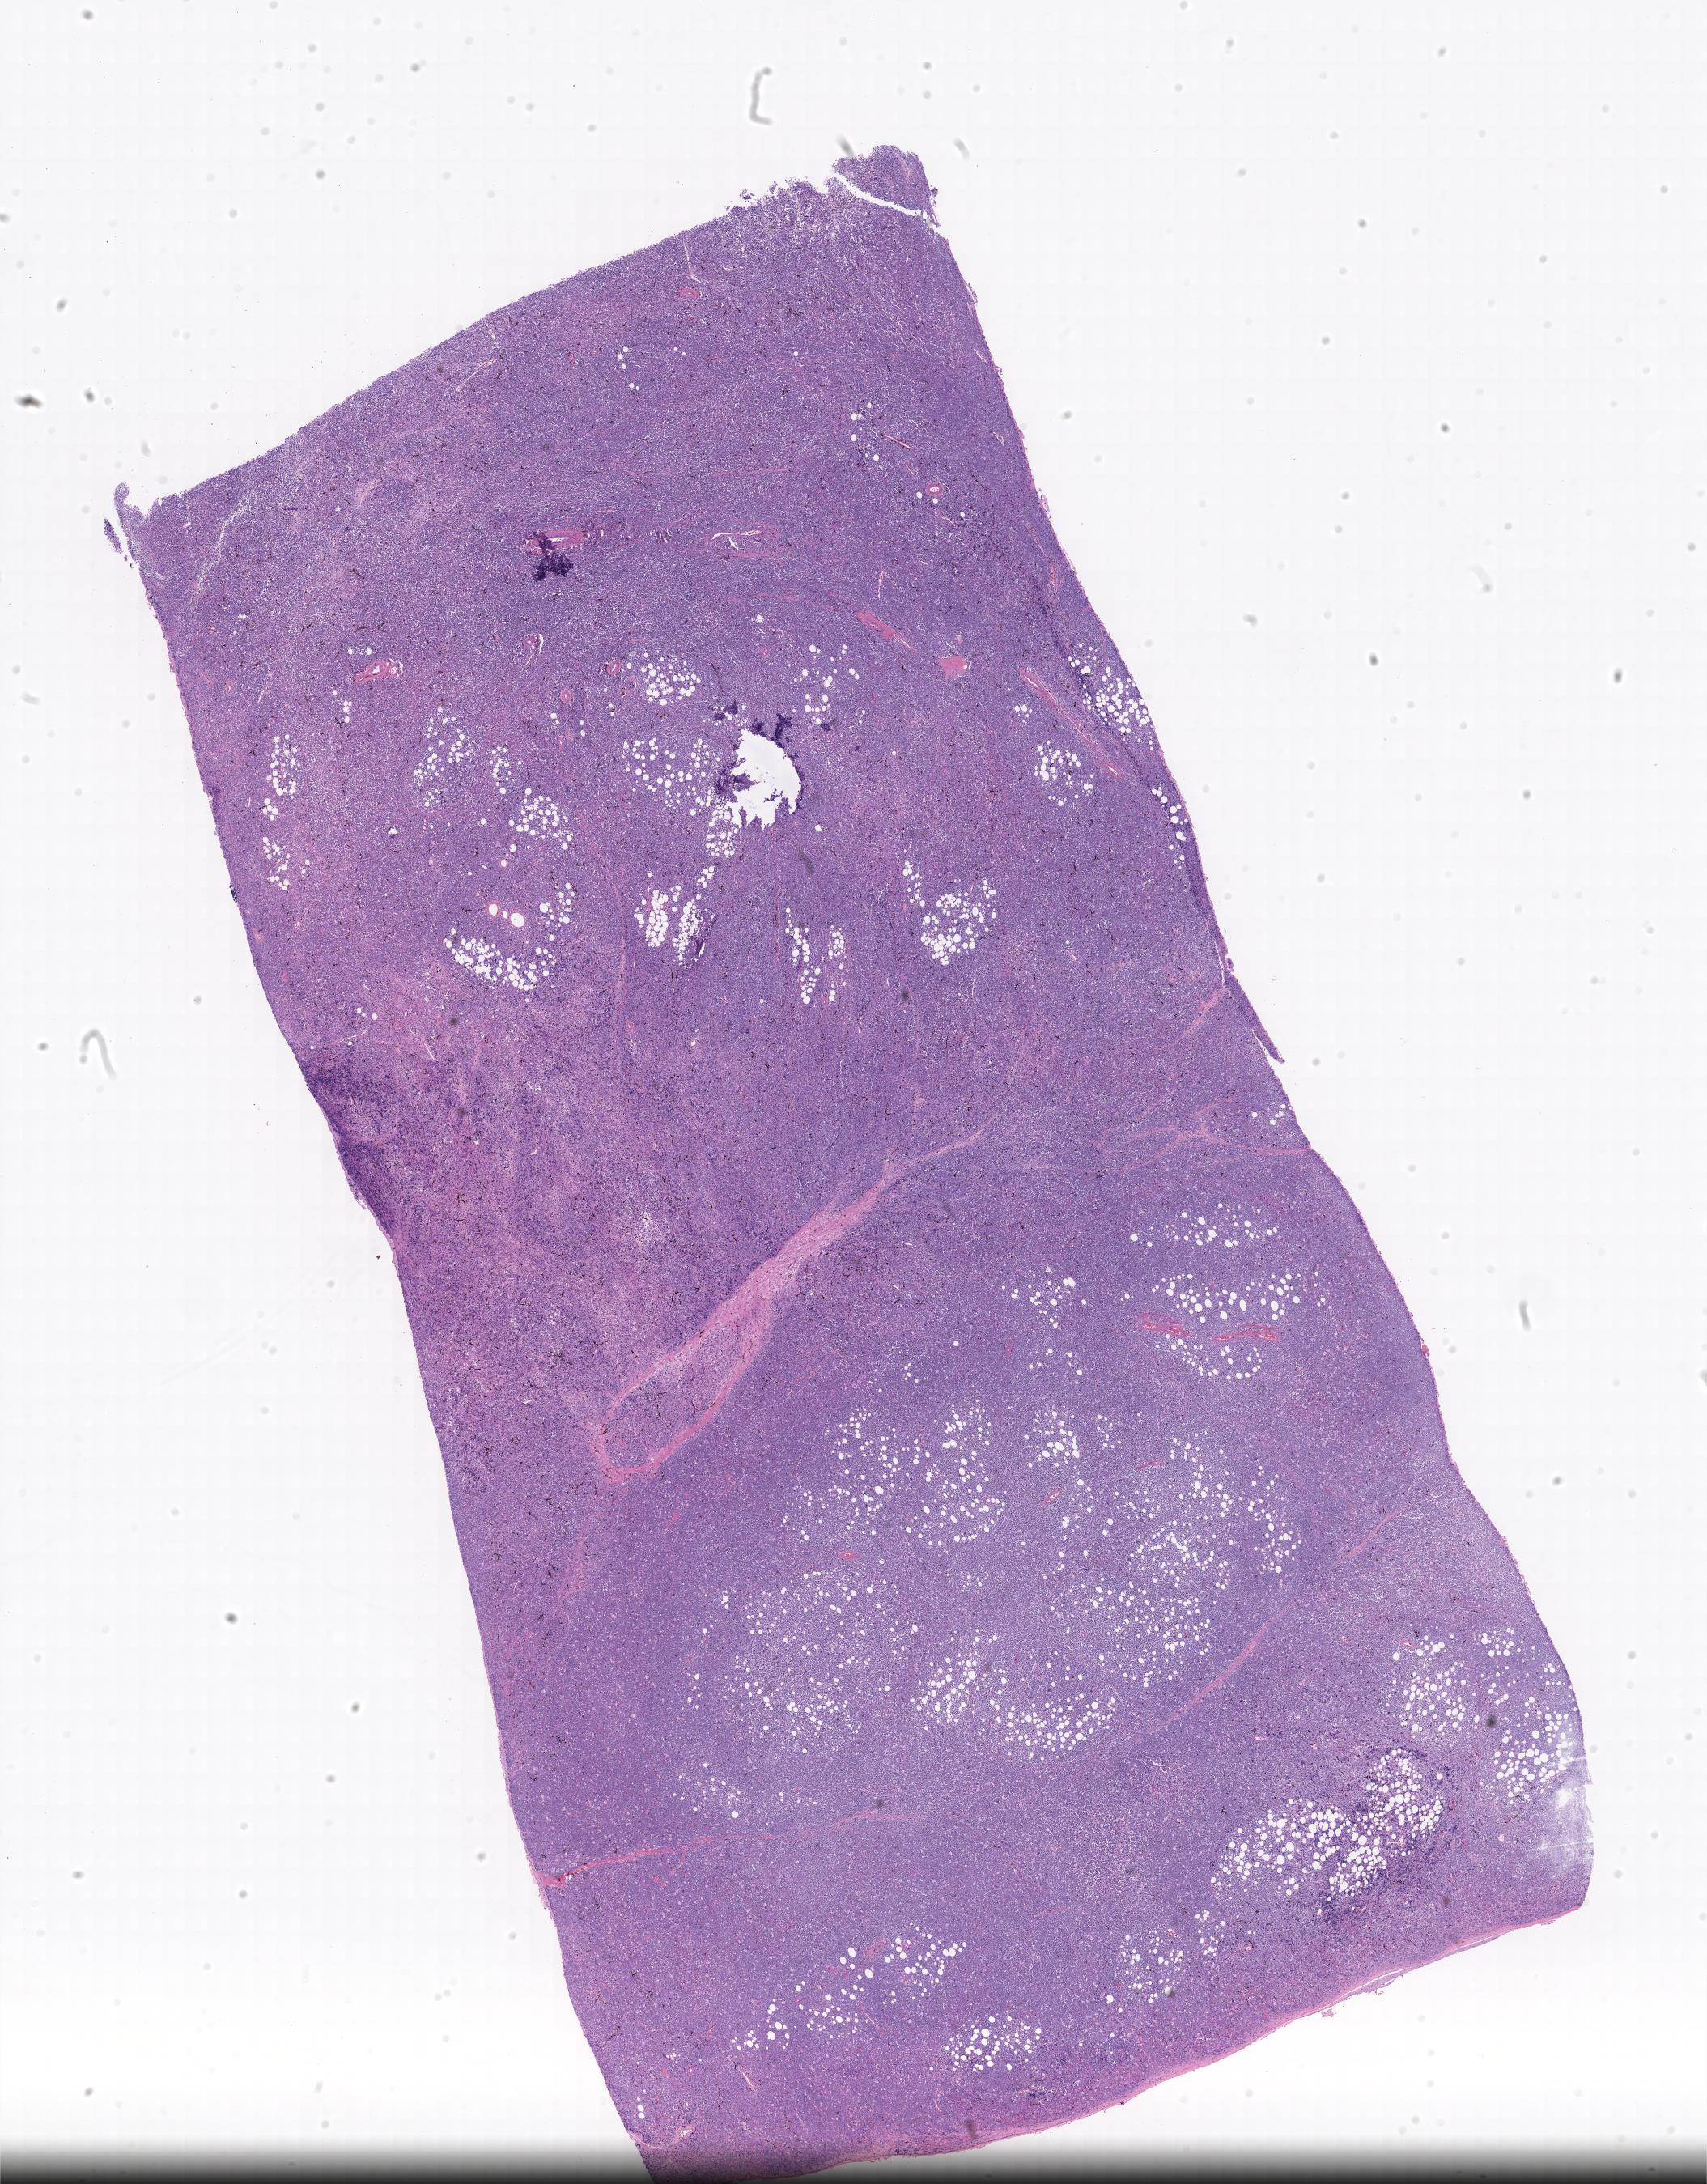
H&E whole-slide image, shown as a low-resolution overview of the whole scanned area. Specimen: tumor tissue. Site: colon. Patient: female, age 12 years.
Diagnosis: Burkitt lymphoma, NOS.